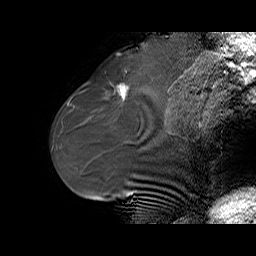
Breast MRI (dynamic contrast-enhanced), one sagittal slice. Slice 24 of 70 in the series (ordered by position). Dynamic contrast-enhanced series, time point 2 of 6 at this slice position (early post-contrast). 1.5 T. TE 5.5 ms, TR 32.9 ms. 256 × 256 image matrix. Female patient. Case-level facts recorded for this patient, not image findings: setting: breast cancer imaged before/during neoadjuvant chemotherapy; receptor status: HER2-positive.
Annotated regions visible in this slice (semi-automatically segmented with operator editing):
- analysis volume of interest (the breast-tissue region the enhancement analysis was run in; not a lesion): bounding box [x1, y1, x2, y2] px = [96, 73, 141, 111]
- tumour enhancement mask (voxels above the 100 % enhancement threshold inside the analysis volume of interest): [118, 83, 125, 100]